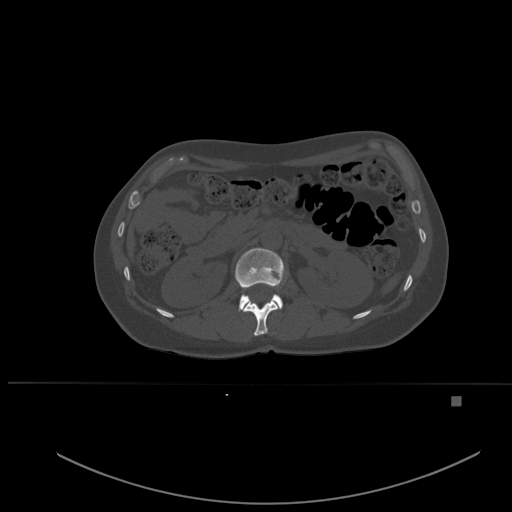
CT including the spine, one axial slice; slice 243 of 651 in the series (ordered by position); bone window (W 1800 / L 400 HU); 1.5 mm slice thickness; 512 × 512 image matrix, field of view 443 × 443 mm. Patient: female, 49 years. Case-level facts recorded for this patient, not image findings: primary cancer: breast.
Outlined on this slice (semi-automatic segmentation, software-assisted and operator-edited):
- L1 vertebra: bounding box <235,248,285,311> (left, top, right, bottom; pixels)
- T12 vertebra: <243,300,278,336>